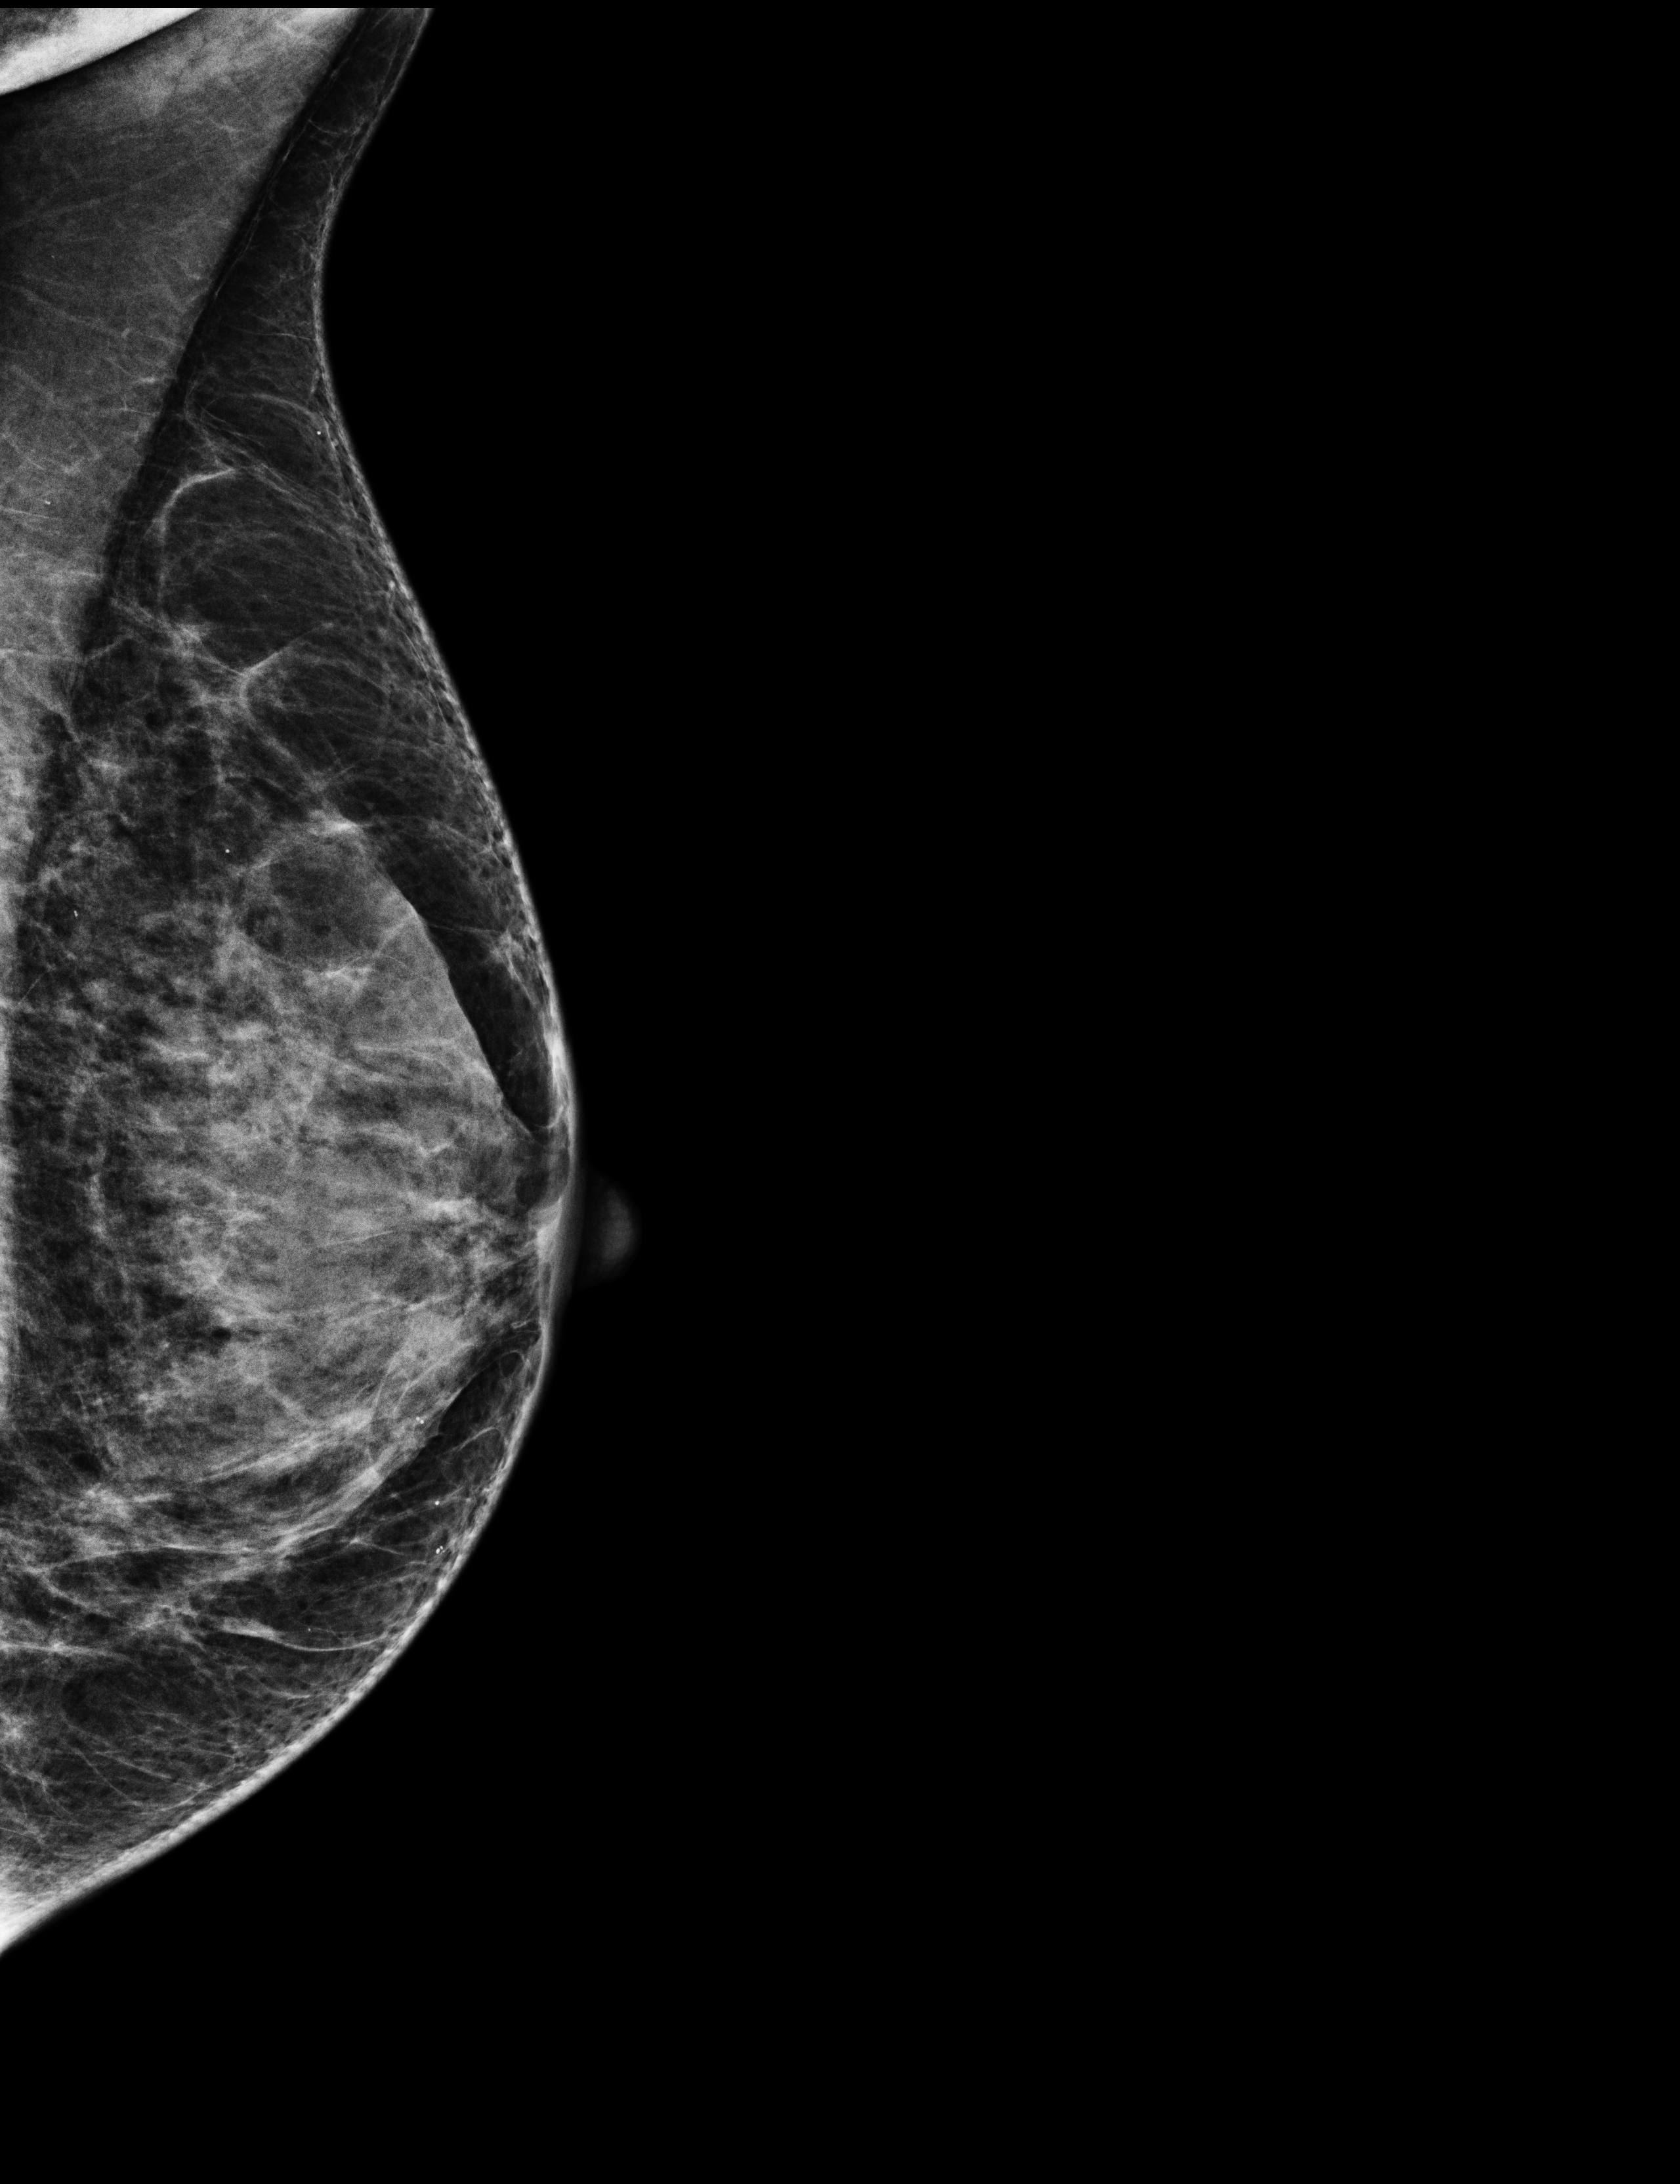
Screening examination. Patient: female, 56 years.
Image type: full-field digital mammogram. Breast: left. Projection: medio-lateral oblique projection.